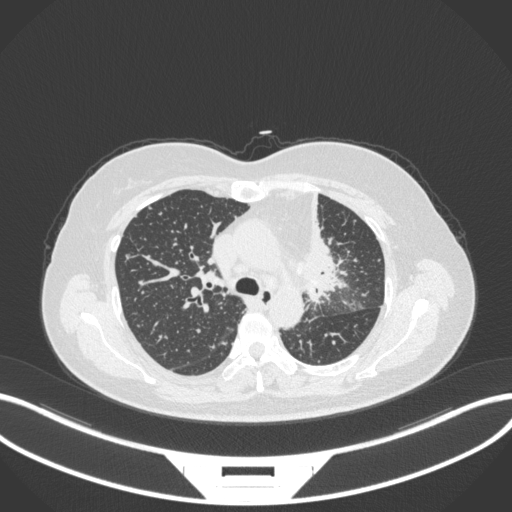
Chest CT, one axial slice; position 227 of 348 along the scan axis; reconstruction kernel B31f; 120 kVp; lung window (W 1500 / L -600 HU); 1 mm slice thickness; 512 × 512 image matrix, field of view 400 × 400 mm. Patient: female, 49 years. From the clinical record (not read from this slice): clinical TNM (as recorded): T1c N0 M1.
Structures marked on this image (rectangle marked by the reading radiologist):
- lung tumour (recorded histology: adenocarcinoma): box from (x=294, y=193) to (x=351, y=311) px